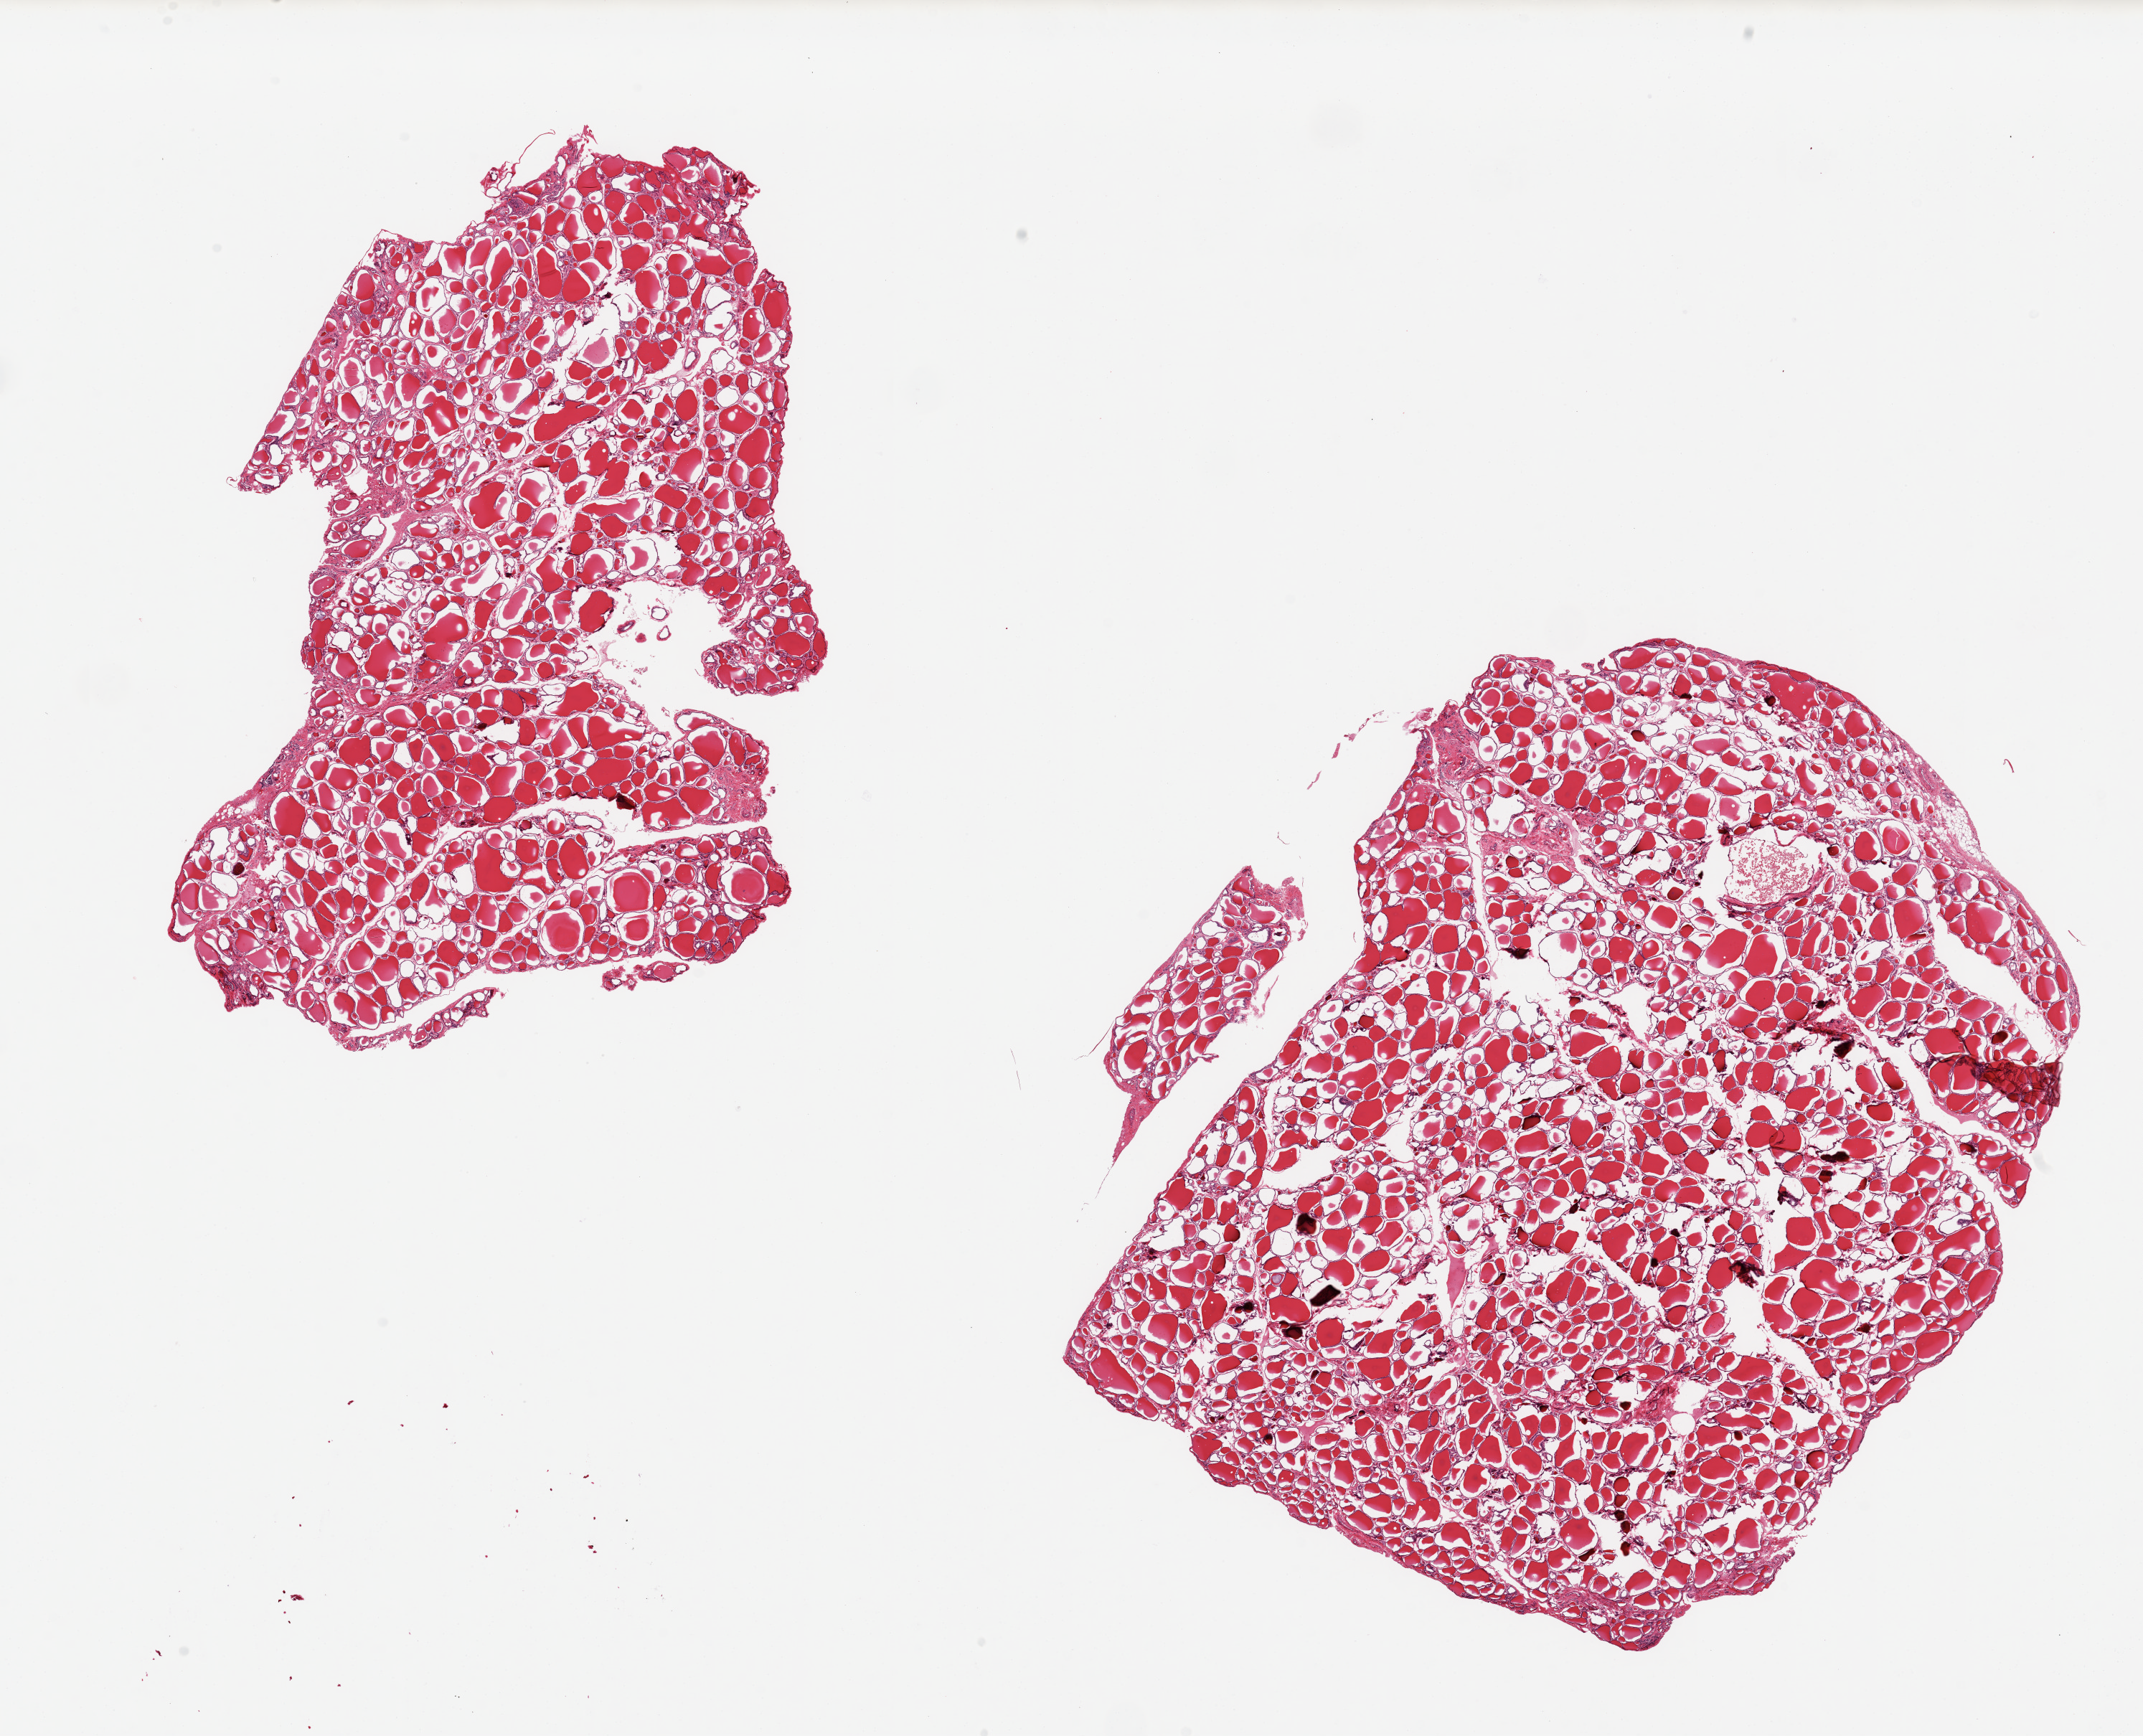
Hematoxylin and eosin (H&E) whole-slide image, whole scanned area (about 23.6 x 19.1 mm) shown as a low-resolution overview. PAXgene-fixed paraffin-embedded (PFPE) section. Section of thyroid (target tissue). Donor tissue sample. Donor: male.
Reviewer comment on this tissue sample: 2 pieces ~10x7mm.